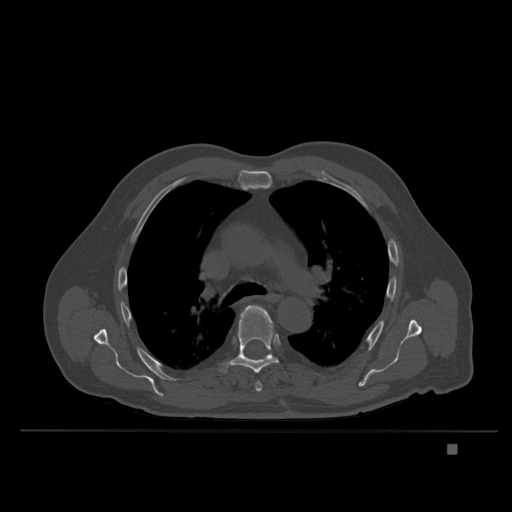
CT including the spine, one axial slice; slice 261 of 435 in the series (ordered by position); bone window (W 1800 / L 400 HU); 512 × 512 image matrix, field of view 434 × 434 mm. Male patient, age 73 years. Case-level facts recorded for this patient, not image findings: primary cancer: skin.
Outlined on this slice (semi-automatic segmentation, software-assisted and operator-edited):
- T5 vertebra: bounding box (x1, y1, x2, y2) in pixels: (255, 381, 262, 392)
- T6 vertebra: (220, 305, 279, 373)